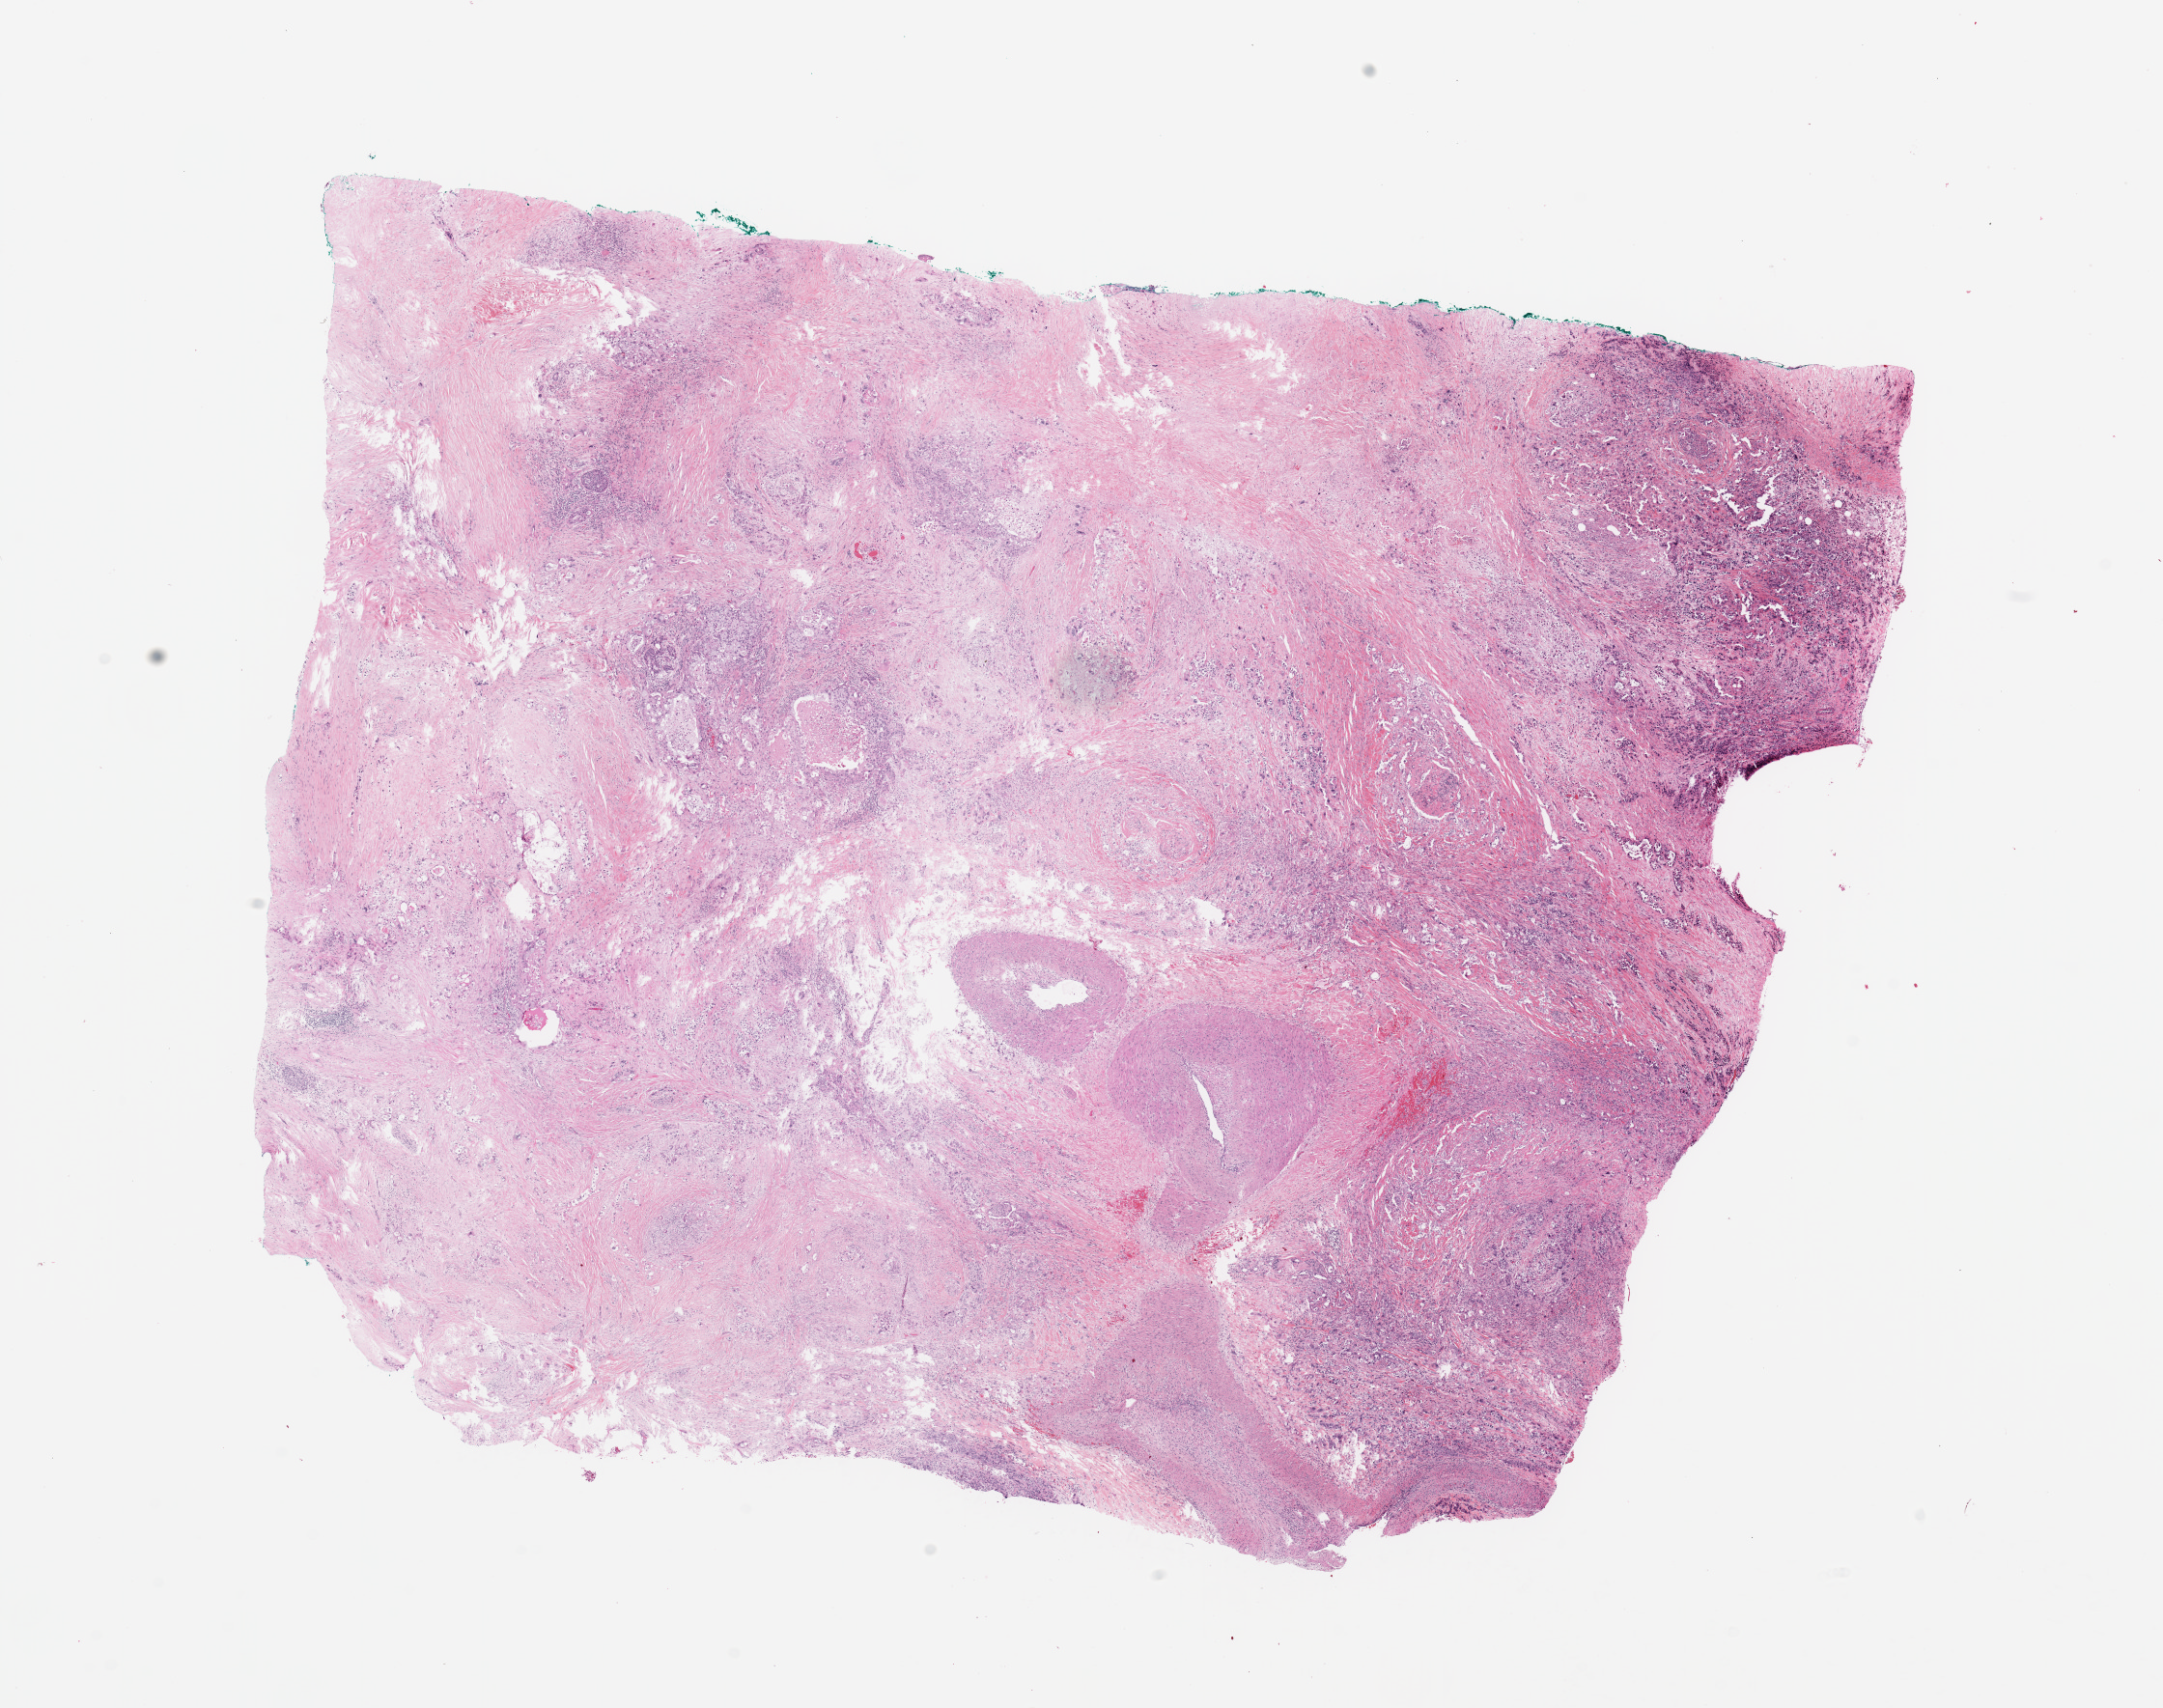
H&E-stained whole-slide image — a low-resolution overview of the entire scanned area, about 17.7 x 14.0 mm. Tumour tissue sample, sampled site: pancreas. Male, 42 y/o. Histologic grade: G4 (undifferentiated). Composition of this section per pathologist review: tumour nuclei 60%, necrosis 5%.
AJCC pathologic stage: IIB. Diagnosis: Infiltrating duct carcinoma, NOS. Primary tumour site (as recorded): head.